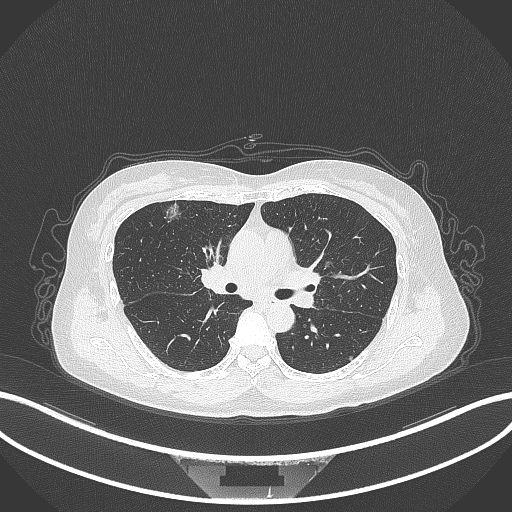
Chest CT, one axial slice; slice 196 of 315 in the series (ordered by position); reconstruction kernel B70f; 120 kVp; lung window (W 1500 / L -600 HU); 1 mm slice thickness; 512 × 512 image matrix. Female patient, age 61 years. Case-level facts recorded for this patient, not image findings: clinical TNM (as recorded): T1b N0 M0.
Annotated regions visible in this slice (rectangle marked by the reading radiologist):
- lung tumour (recorded histology: adenocarcinoma): box from (x=159, y=199) to (x=184, y=227) px